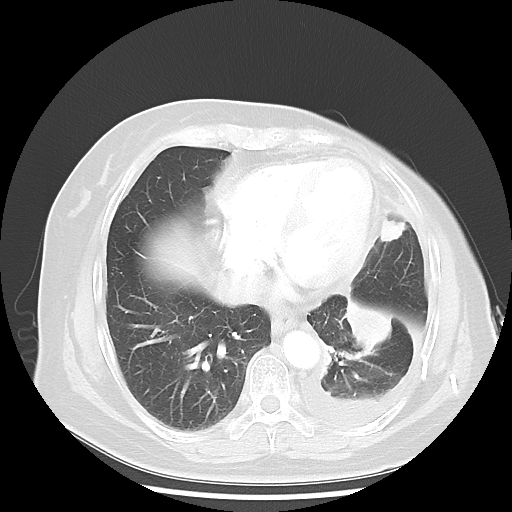
Chest CT, one axial slice; reconstruction kernel LUNG; 120 kVp; lung window (W 1500 / L -600 HU); 5 mm slice thickness; 512 × 512 image matrix, field of view 360 × 360 mm. Female patient, age 63 years. From the clinical record (not read from this slice): clinical TNM (as recorded): T2 N0 M1.
Annotated regions visible in this slice (rectangle marked by the reading radiologist):
- lung tumour (recorded histology: adenocarcinoma): bounding box [x1, y1, x2, y2] px = [340, 298, 391, 355]